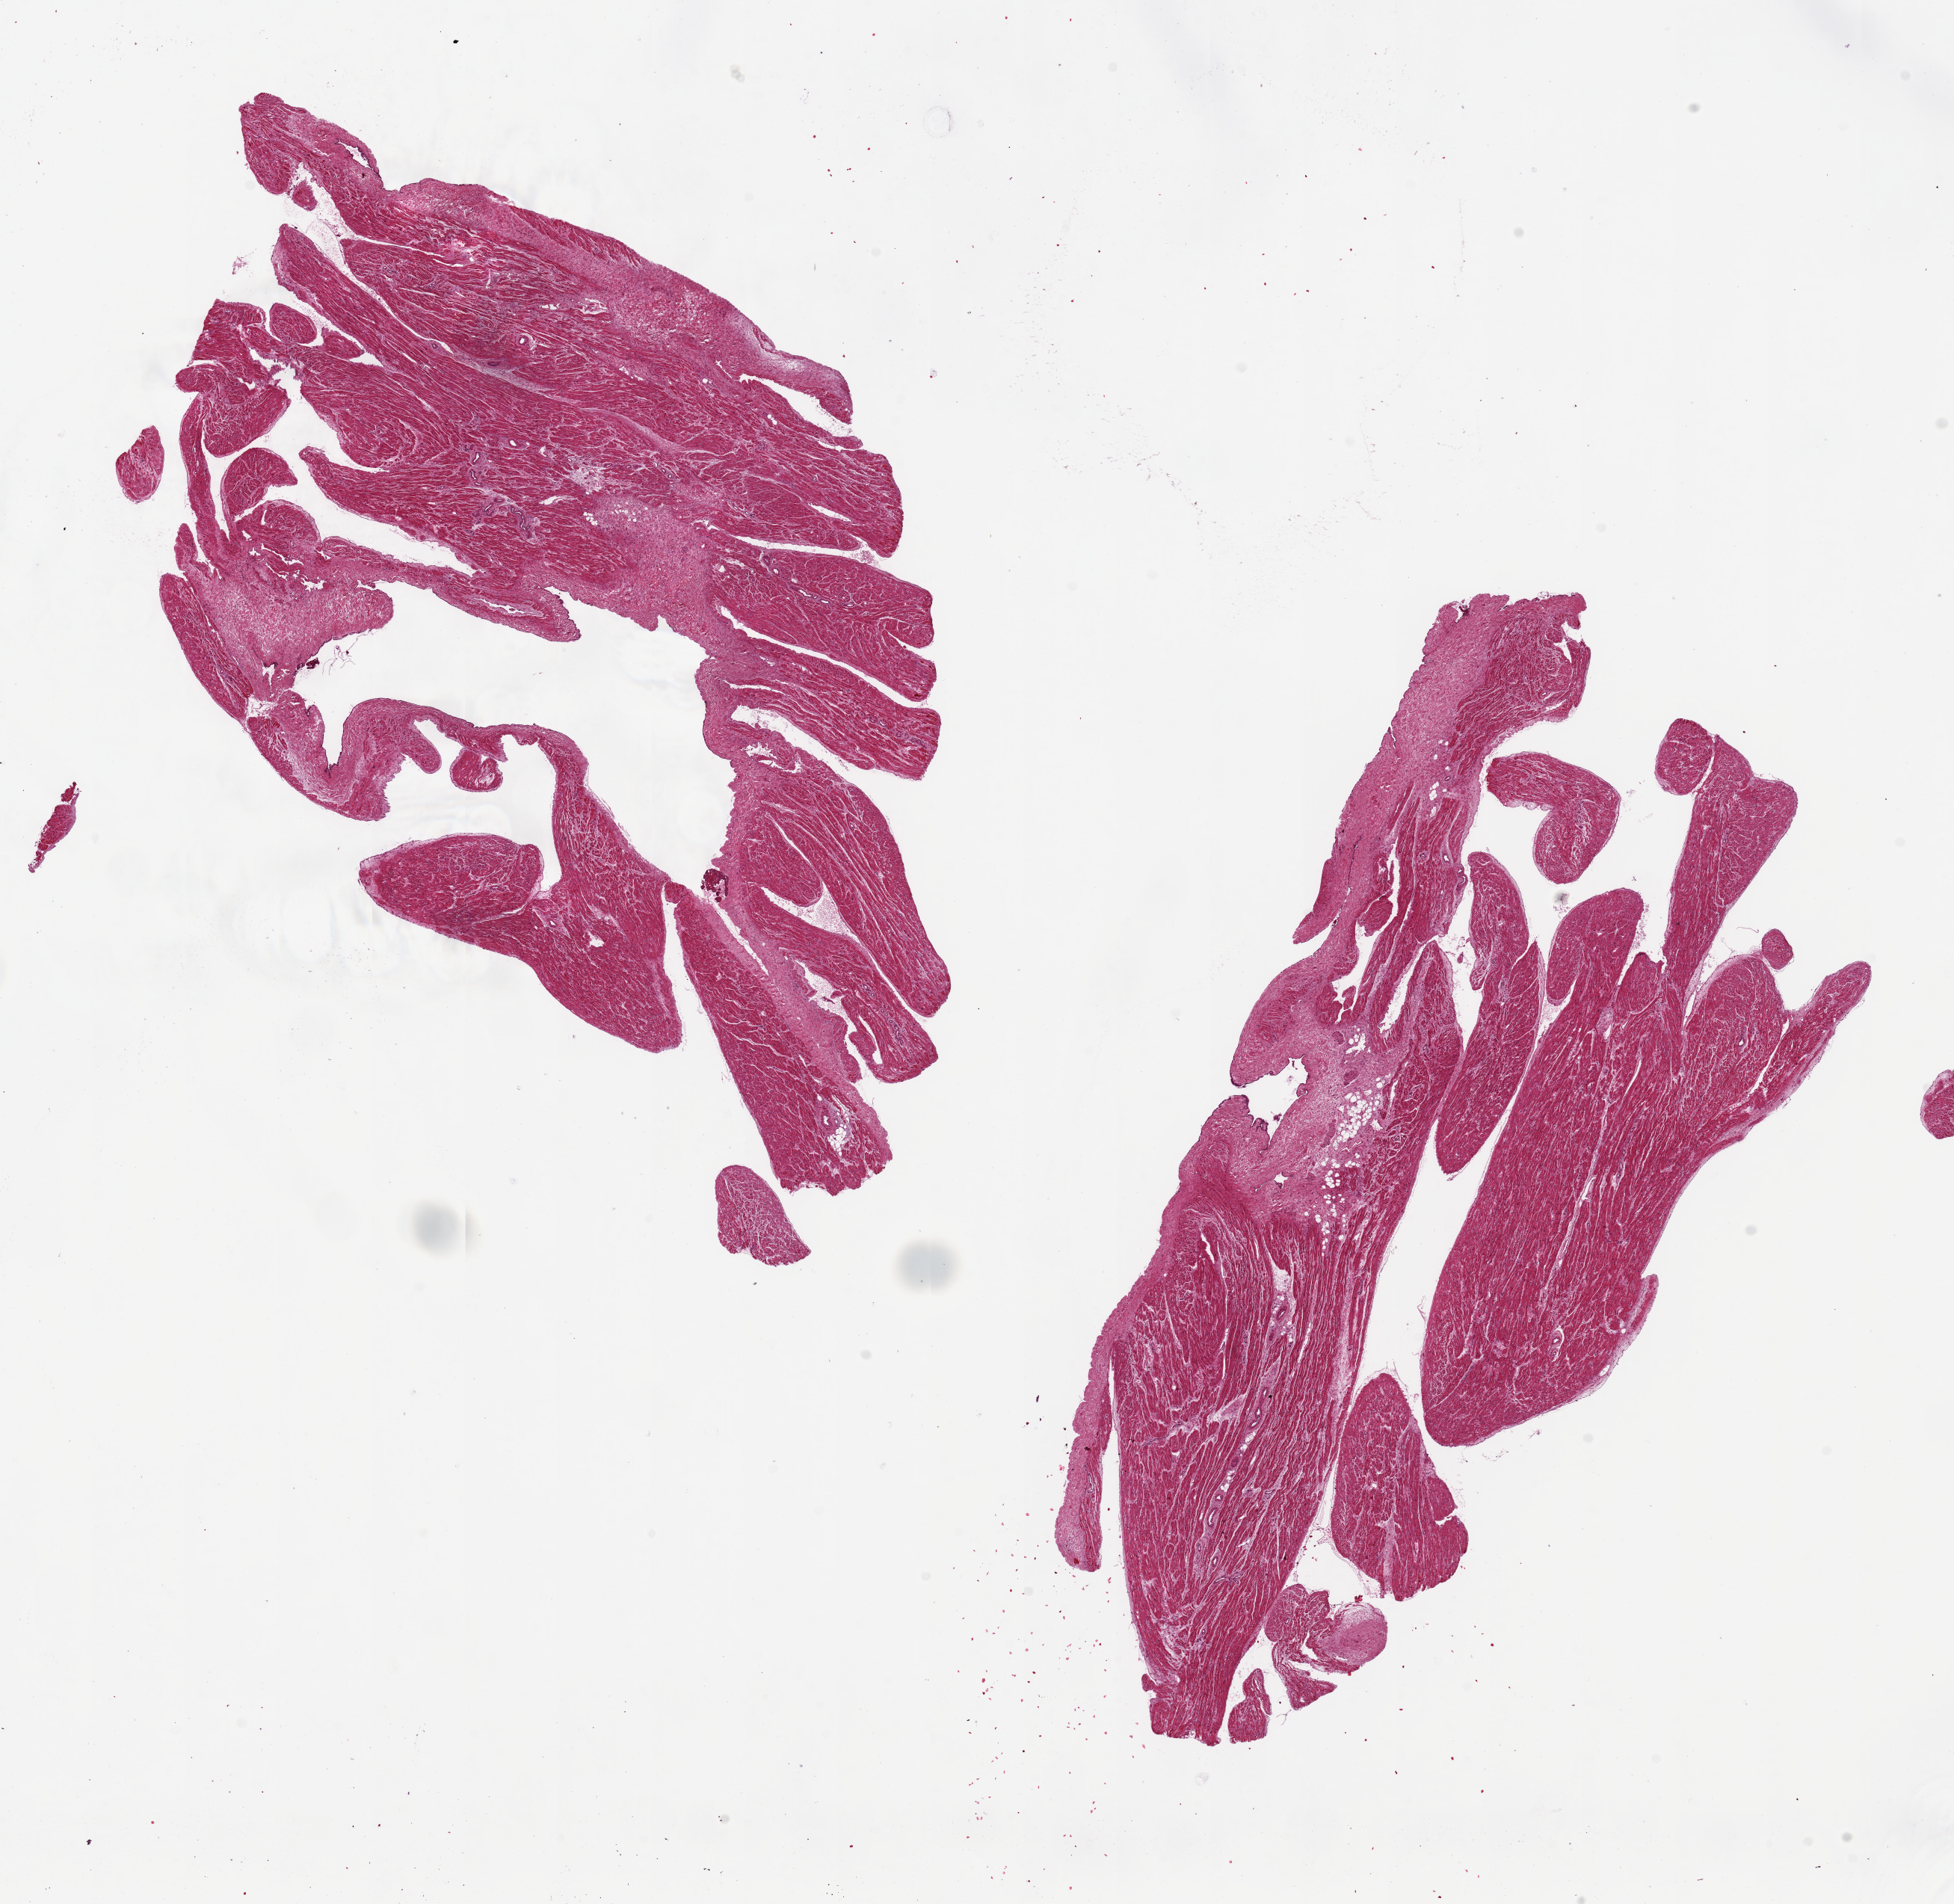
Haematoxylin and eosin whole-slide image — low-resolution overview of the scanned area, about 20.7 x 20.1 mm (from a 20x scan), PAXgene-fixed paraffin-embedded (PFPE) section, section of auricular appendage (target tissue), donor tissue sample.
• reviewer comment on this tissue sample: 2 pieces ~10x6mm